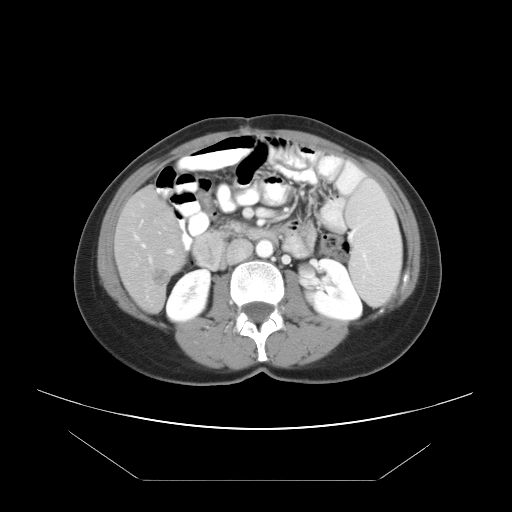
Contrast-enhanced abdominal CT, one axial slice; position 15 of 45 along the scan axis; reconstruction kernel STANDARD; intravenous contrast given; soft-tissue window (W 400 / L 40 HU); 5 mm slice thickness; 512 × 512 image matrix, field of view 405 × 405 mm. Female patient, age 52 years. From the clinical record (not read from this slice): diagnosis: colorectal cancer liver metastases, imaged before liver resection; multiple liver metastases: yes; largest metastasis: 2.5 cm; disease in both lobes: no.
Outlined on this slice (expert manual segmentation):
- hepatic veins: bounding box [x1, y1, x2, y2] px = [136, 236, 145, 247]
- liver: [116, 189, 183, 311]
- planned liver remnant (the part of the liver to remain after resection): [116, 189, 180, 244]
- portal vein (with intrahepatic branches): [140, 219, 174, 254]
- liver metastasis: [154, 268, 168, 287]